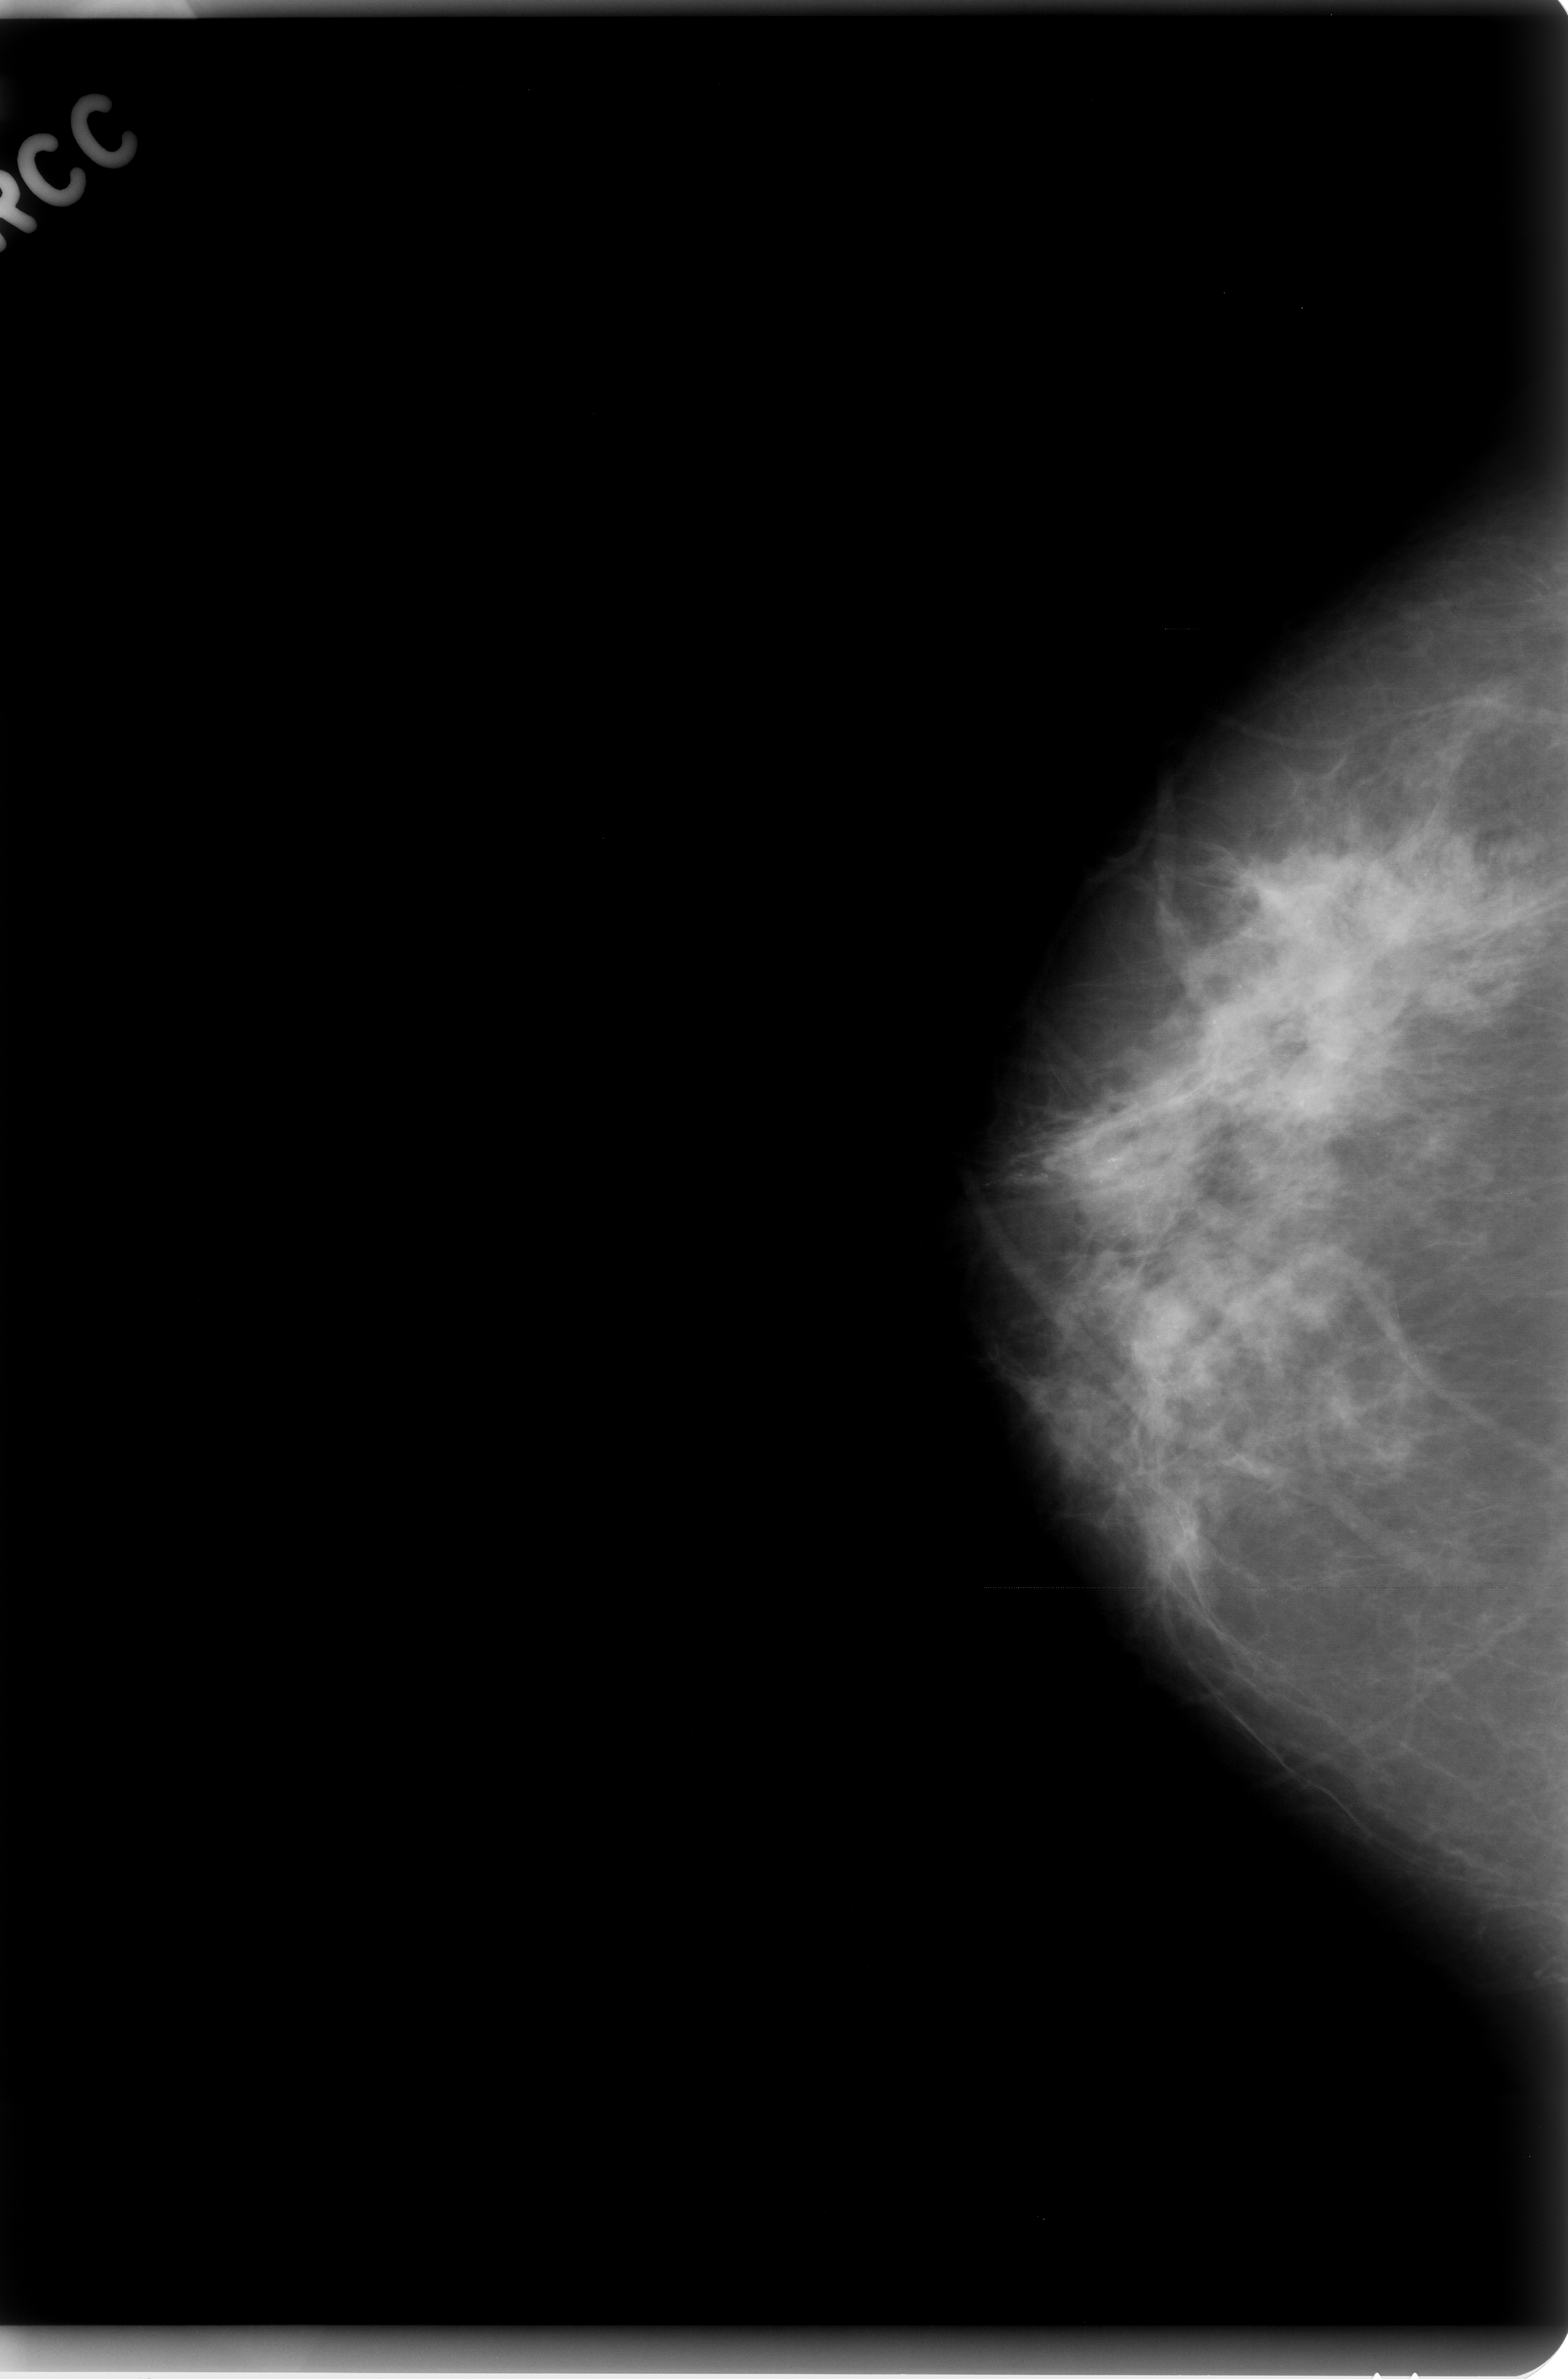
Mammogram (digitized film); right breast; craniocaudal (CC) view; breast composition: scattered fibroglandular densities (BI-RADS density category 2 of 4).
Radiologist-marked abnormalities on this image: calcifications, morphology pleomorphic, distribution regional; BI-RADS assessment category 5; pathology result (as recorded, not read from the image): malignant.